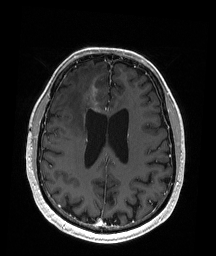
Brain MRI from a brain-tumour surgery series, one axial slice; slice 74 of 192 in the series (ordered by position); T1-weighted post-contrast; 1 mm slice thickness; 216 × 256 image matrix, field of view 211 × 250 mm. Case-level facts recorded for this patient, not image findings: histopathology: Astrocytoma; WHO grade: 3; IDH mutation: yes; tumour location: Right Frontal.
Structures marked on this image (expert manual segmentation):
- tumour: bounding box (x1, y1, x2, y2) in pixels: (91, 92, 97, 110)